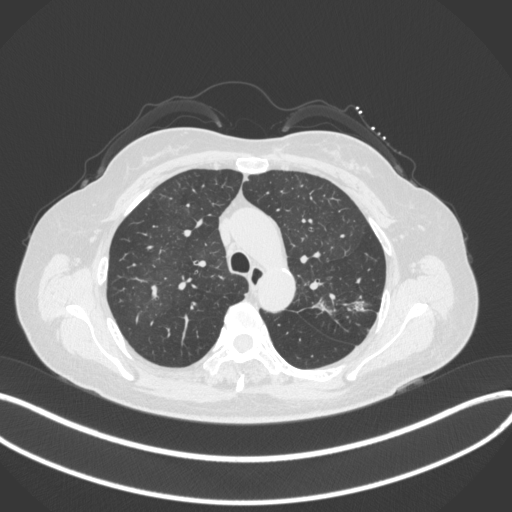
Chest CT, one axial slice; position 249 of 330 along the scan axis; reconstruction kernel B31f; 120 kVp; lung window (W 1500 / L -600 HU); 1 mm slice thickness; 512 × 512 image matrix, field of view 400 × 400 mm. Patient: female, 60 years. Case-level facts recorded for this patient, not image findings: clinical TNM (as recorded): T1c N0 M0.
Annotated regions visible in this slice (rectangle marked by the reading radiologist):
- lung tumour (recorded histology: adenocarcinoma): box from (x=344, y=297) to (x=369, y=317) px